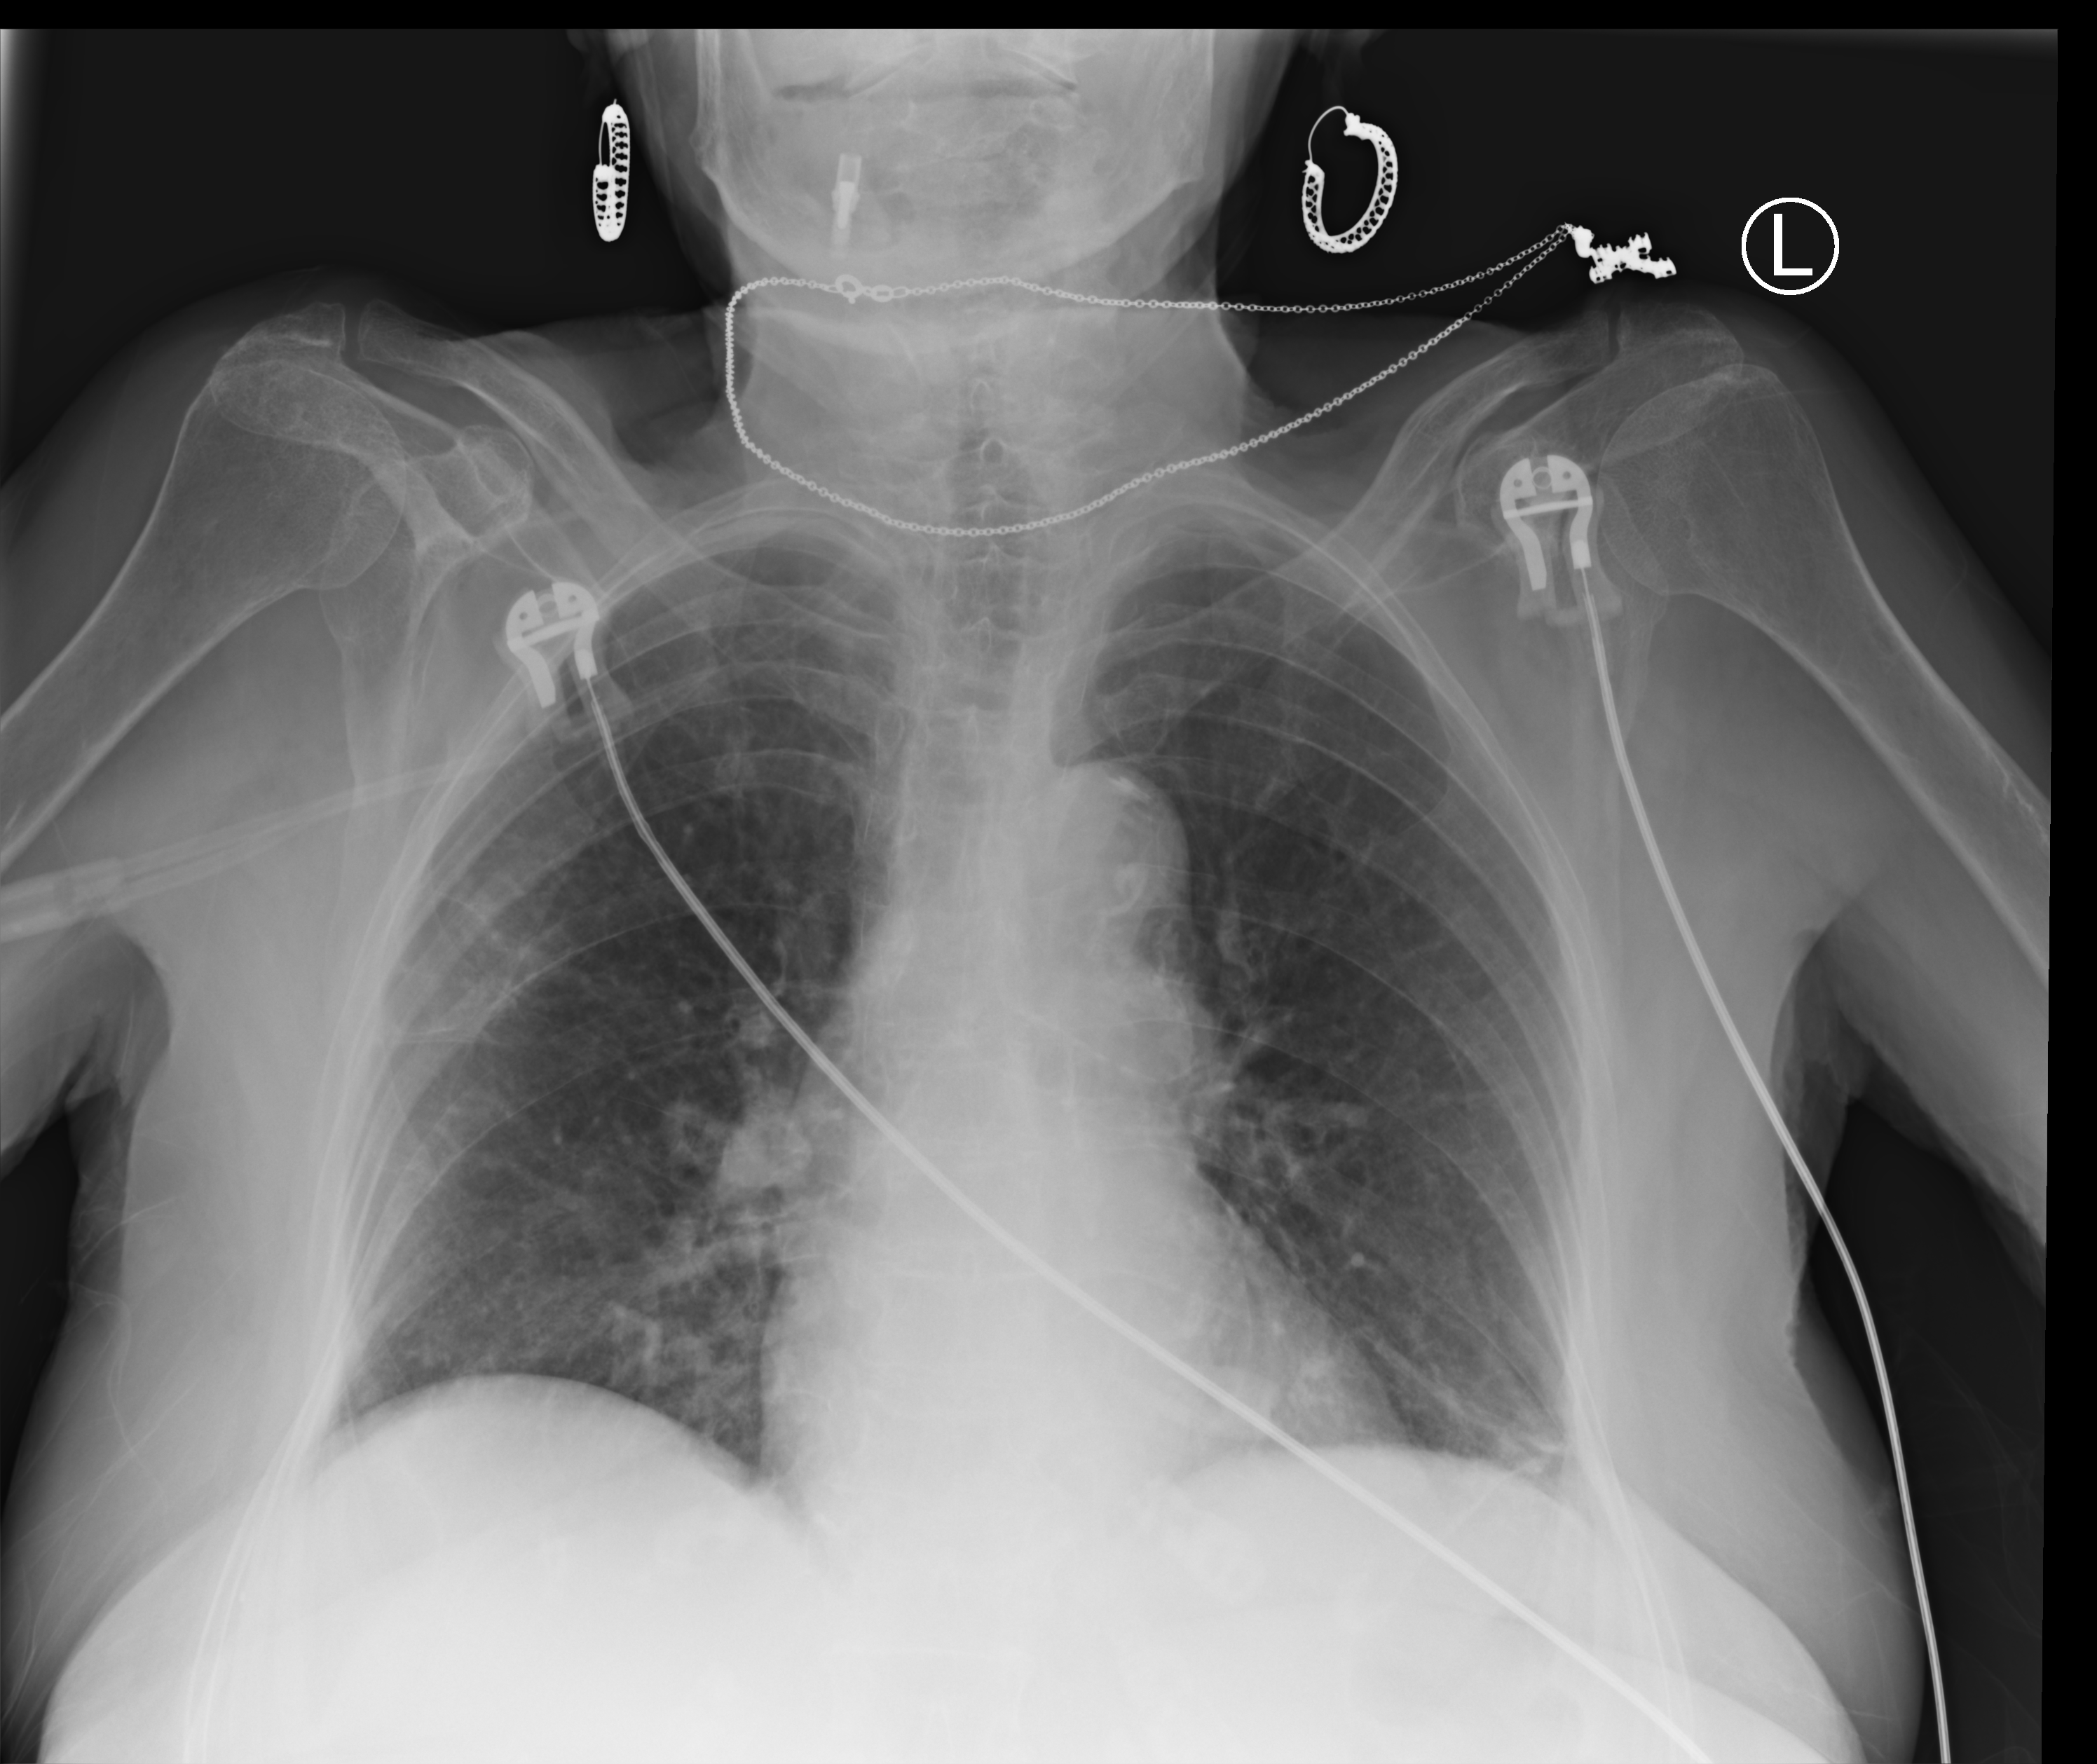
Chest X-ray (portable); anteroposterior (AP) projection. Patient hospitalised with COVID-19; female, aged 75–90 years.
From the hospital-stay record, not from the radiograph (when in the stay this image was taken is not recorded):
- admitted to intensive care during this hospital stay: no
- mechanically ventilated during this hospital stay: no
- COPD (admission record): no